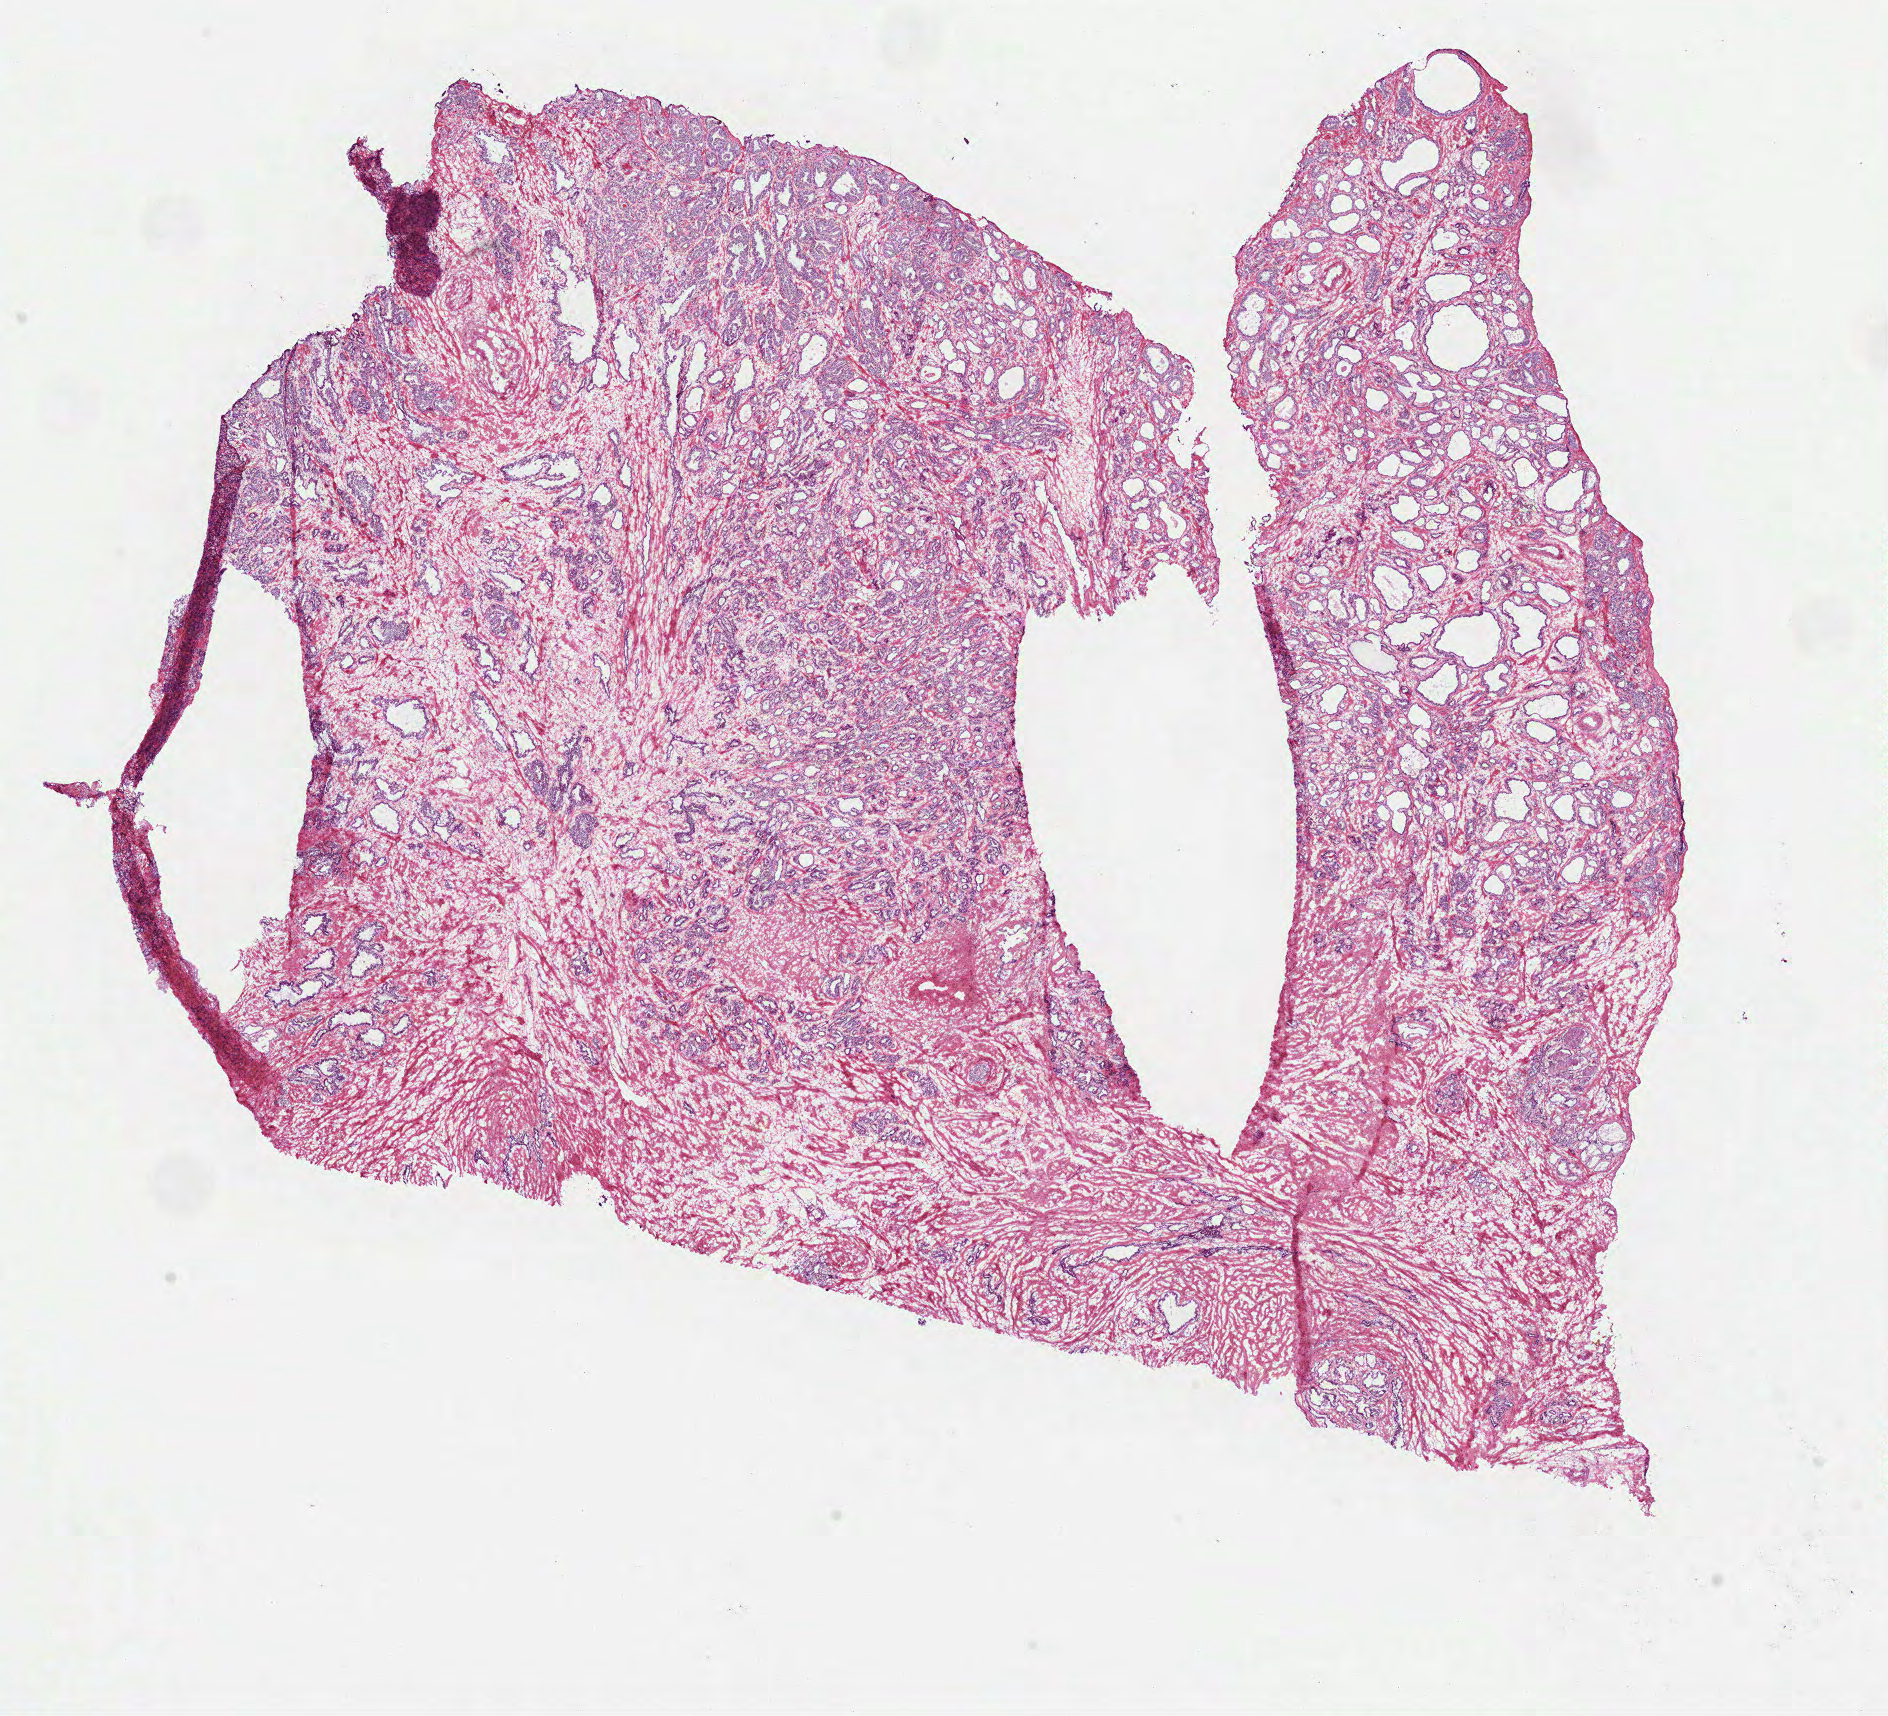
Digitized H&E tissue section (whole slide) — shown as a low-resolution overview of the whole scanned area (about 15.2 x 13.8 mm), frozen section from the bottom of the tissue portion, prostate, primary tumour sample. Male, age 54 years at initial diagnosis. Gleason score: 7 (3+4). Pathologist review of this section (percent, as recorded): tumour cells 40%, tumour nuclei 50%, normal cells 10%, stromal cells 50%, necrosis 0%. Infiltration values recorded for this section: lymphocyte infiltration 0%, monocyte infiltration 0%, neutrophil infiltration 0%.
- lymph nodes positive (case pathology): 0 of 7 examined
- histologic diagnosis: Acinar cell carcinoma (prostate gland)